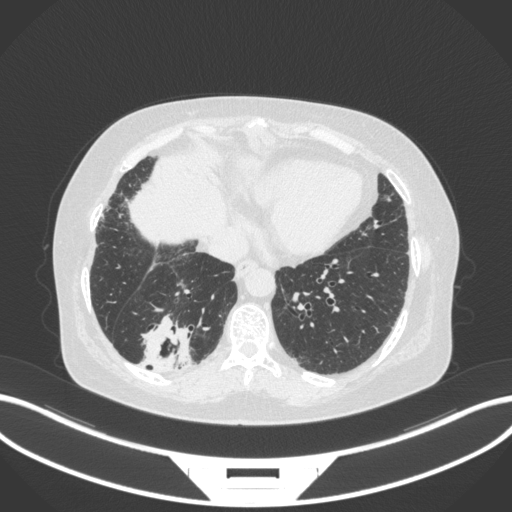
Chest CT, one axial slice; slice 58 of 303 in the series (ordered by position); 120 kVp; lung window (W 1500 / L -600 HU); 1 mm slice thickness; 512 × 512 image matrix, field of view 400 × 400 mm. Female patient, age 65 years. From the clinical record (not read from this slice): clinical TNM (as recorded): T2b N1 M0; histopathological grade: G1.
Structures marked on this image (bounding box drawn by a radiologist):
- lung tumour (recorded histology: adenocarcinoma): bounding box (x1, y1, x2, y2) in pixels: (136, 312, 195, 376)